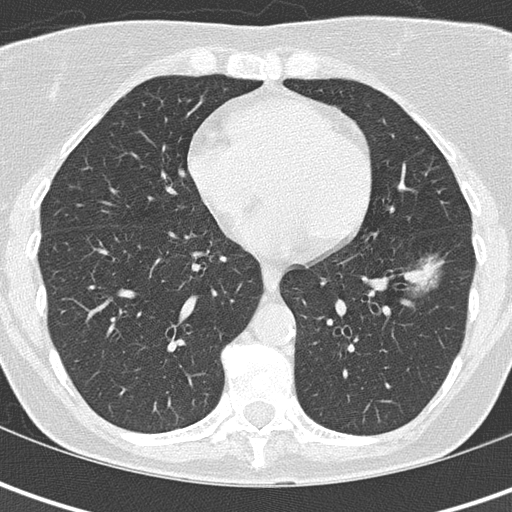
Chest CT (low-dose screening protocol), one axial image; first (baseline) screen; lung window (W 1500 / L -600 HU); 2 mm slice thickness; lung (sharp) reconstruction kernel (B50f); 512 × 512 image matrix, field of view 280 × 280 mm. Female, age 61 years at enrolment. Former smoker at enrolment.
Lesion marked by an expert reader, box from (x=380, y=248) to (x=454, y=305) px. The exam's reader record, not a measurement of the box and not confirmed to be the same lesion: non-calcified nodule or mass ≥4 mm, left lower lobe, 29 × 16 mm, ground glass attenuation. Official screen result: positive, change unspecified: nodule(s) >= 4 mm or enlarging nodule(s), mass(es), or other non-specific abnormalities suspicious for lung cancer. Lung cancer was diagnosed 259 days after this screen: bronchiolo-alveolar adenocarcinoma, NOS, left lower lobe, well differentiated (G1), stage IA (AJCC 6th edition), 10 mm at pathology.